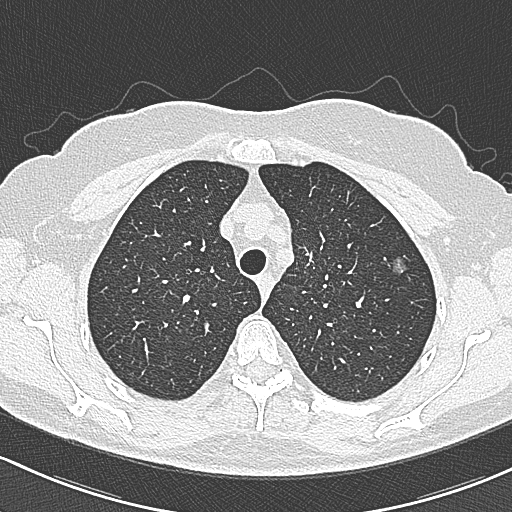
Axial slice from a low-dose chest CT screening exam, baseline screening round, lung window (W 1500 / L -600 HU), 1 mm slice thickness, lung (sharp) reconstruction kernel (B80f), 120 kVp, slice 67 of 312 in the series, 512 × 512 image matrix. Female, age 65 years at enrolment. Current smoker at enrolment.
• Expert-annotated lung lesion, box from (x=382, y=252) to (x=418, y=286) px.
• The screening reader recorded 3 non-calcified nodules or masses ≥4 mm on this exam (left upper lobe, left upper lobe, right upper lobe); which of them this box marks is not recorded.
• Later outcome: lung cancer diagnosed 390 days after this screen — bronchiolo-alveolar carcinoma, non-mucinous, left upper lobe, stage IA (AJCC 6th edition), 10 mm at pathology.